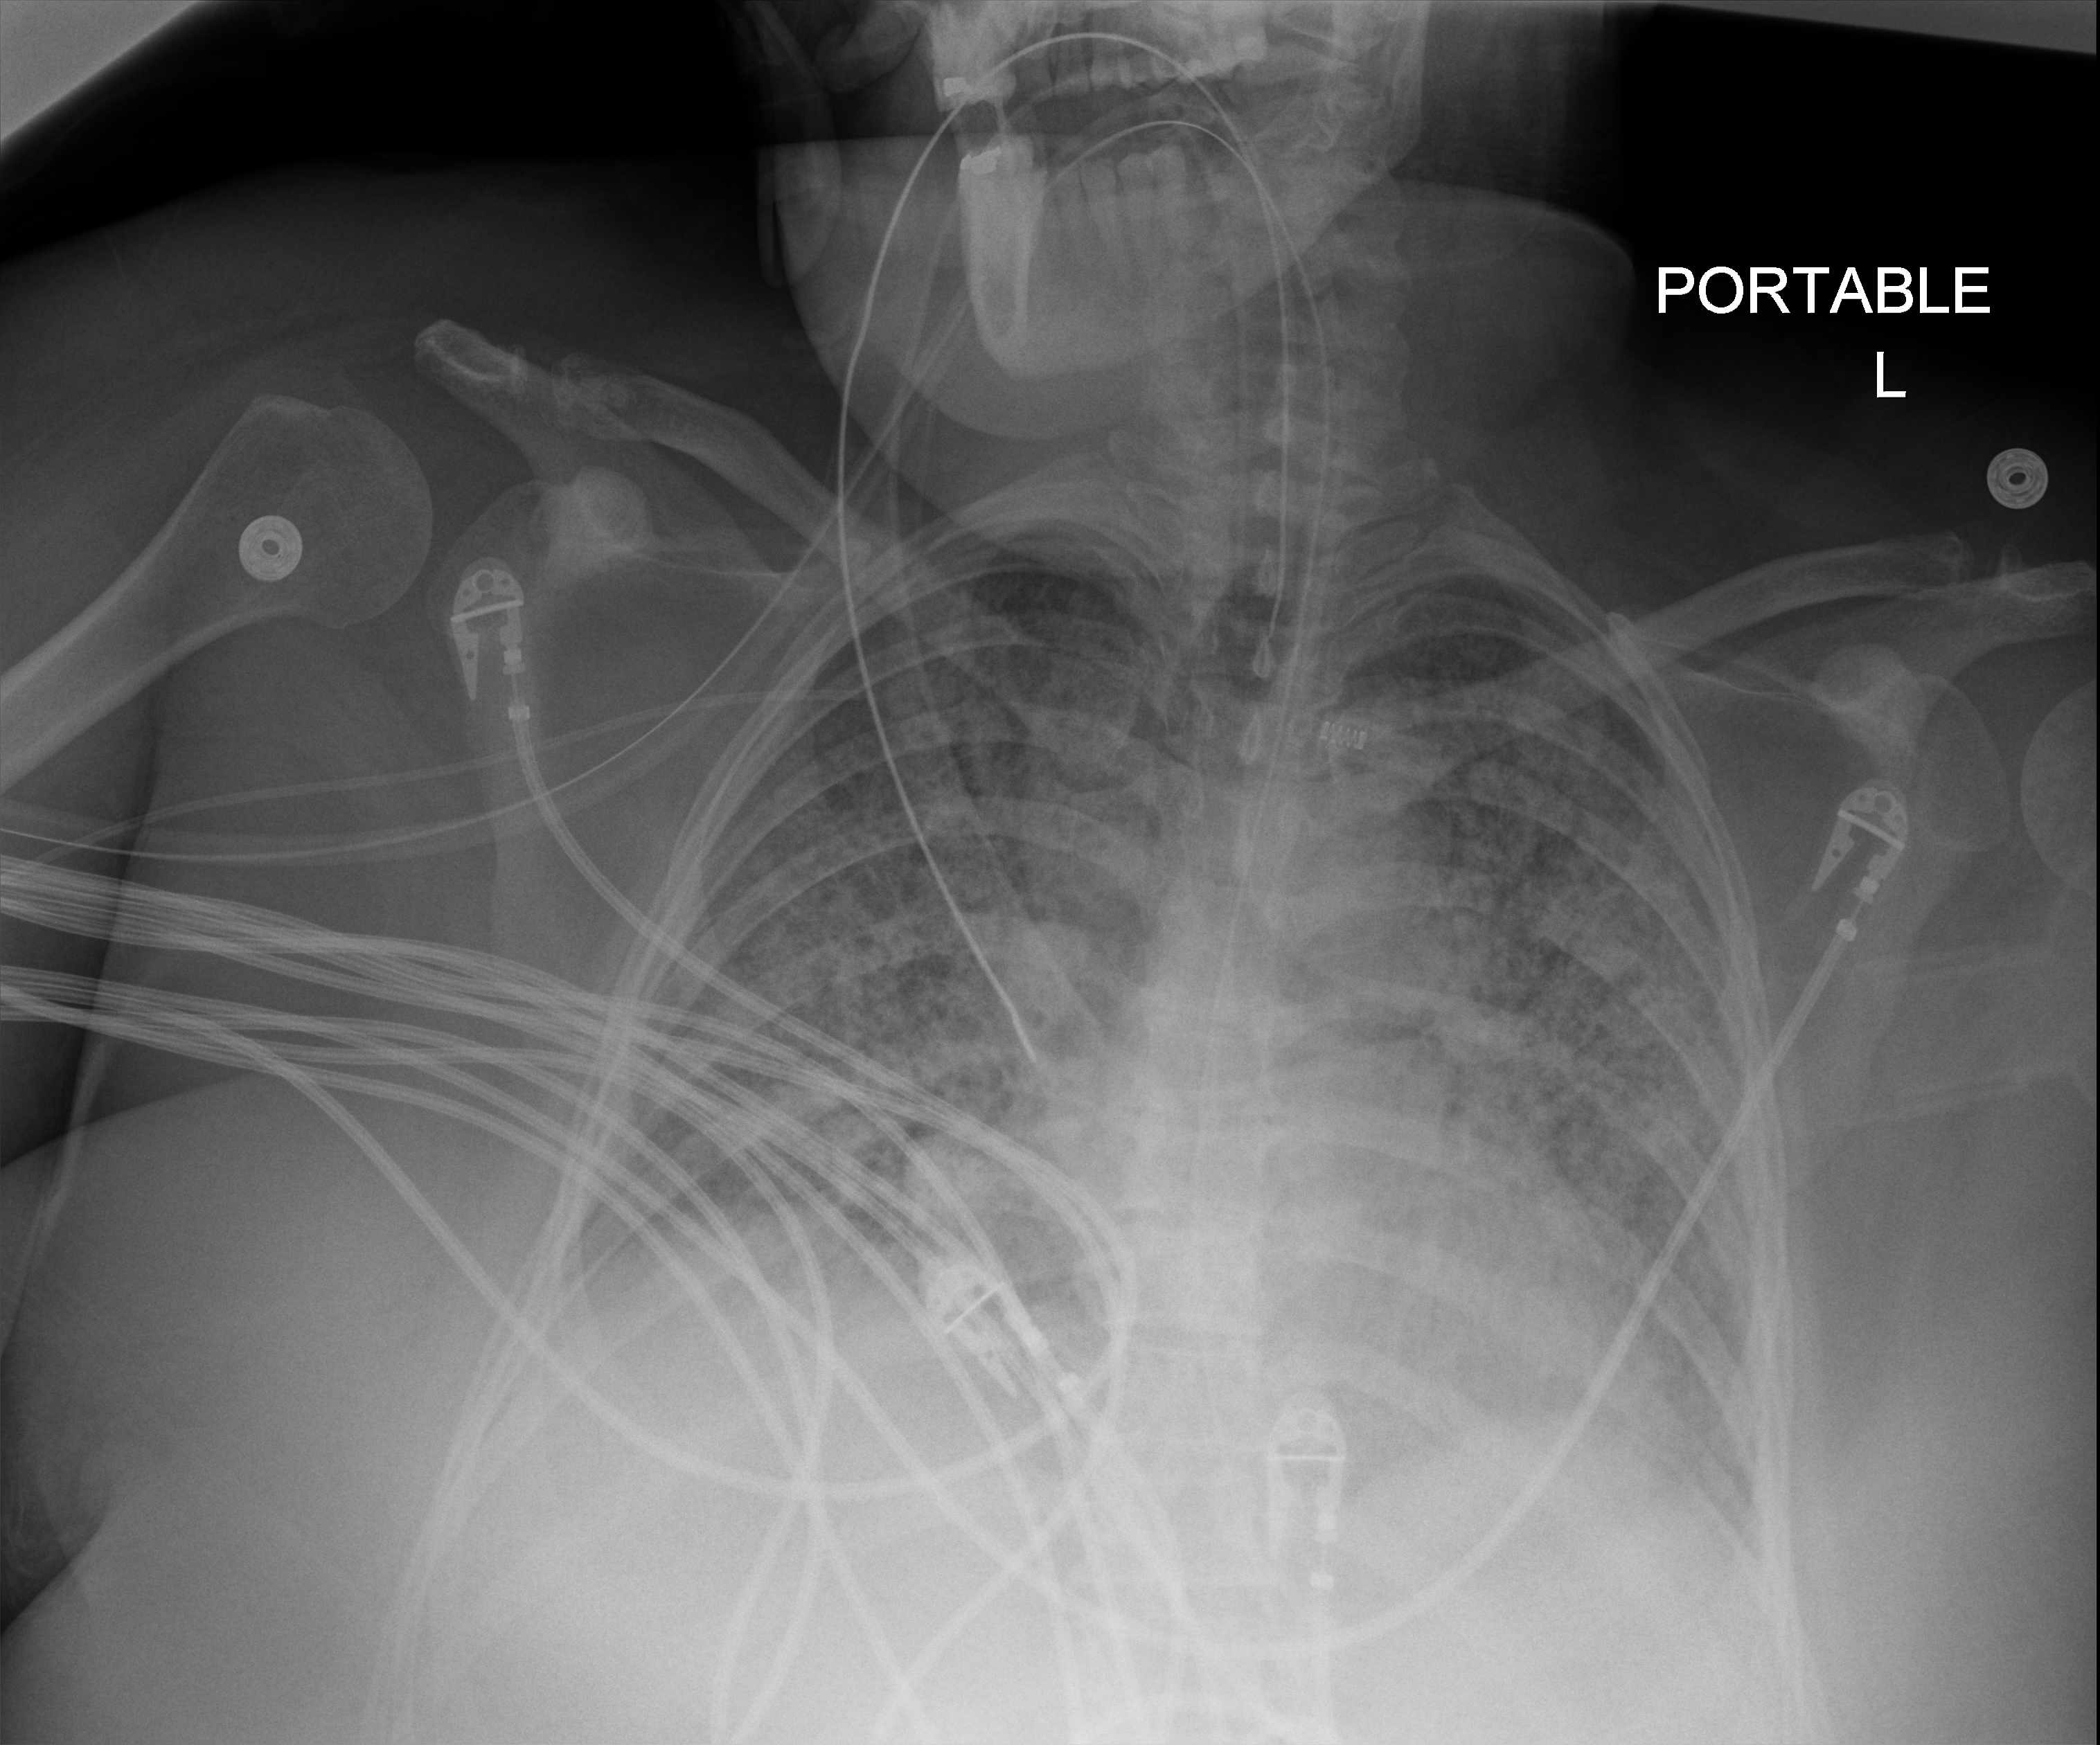
Chest radiograph (digital radiography); anteroposterior (AP) projection. Female patient hospitalised with COVID-19, age 18–59 years.
Hospital-stay facts (about this admission, not read from this image; timing relative to this image not recorded): mechanically ventilated during this hospital stay: yes; admitted to intensive care during this hospital stay: yes.